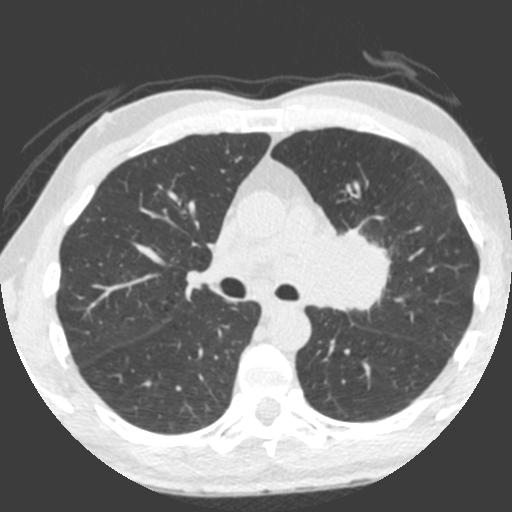
Low-dose screening chest CT, axial slice; third annual screen; lung window (W 1500 / L -600 HU); 2 mm slice thickness; standard (soft-tissue) reconstruction kernel (B); 120 kVp; 512 × 512 image matrix. Male participant, aged 55 years at enrolment. Current smoker at enrolment.
Lesion marked by an expert reader, bounding box [x1, y1, x2, y2] px = [309, 219, 397, 324]. Reader record for this screening exam (exam-level; its link to the box is not recorded): non-calcified nodule or mass ≥4 mm, left upper lobe, 49 × 29 mm, spiculated (stellate) margins, soft tissue attenuation, pre-existing on the prior screen: yes; interval growth: yes. Official screen result: positive, other. Participant outcome: lung cancer diagnosed 0 days after this screen — small cell carcinoma, NOS, left upper lobe, undifferentiated (G4), stage IV (AJCC 6th edition), 60 mm at pathology.